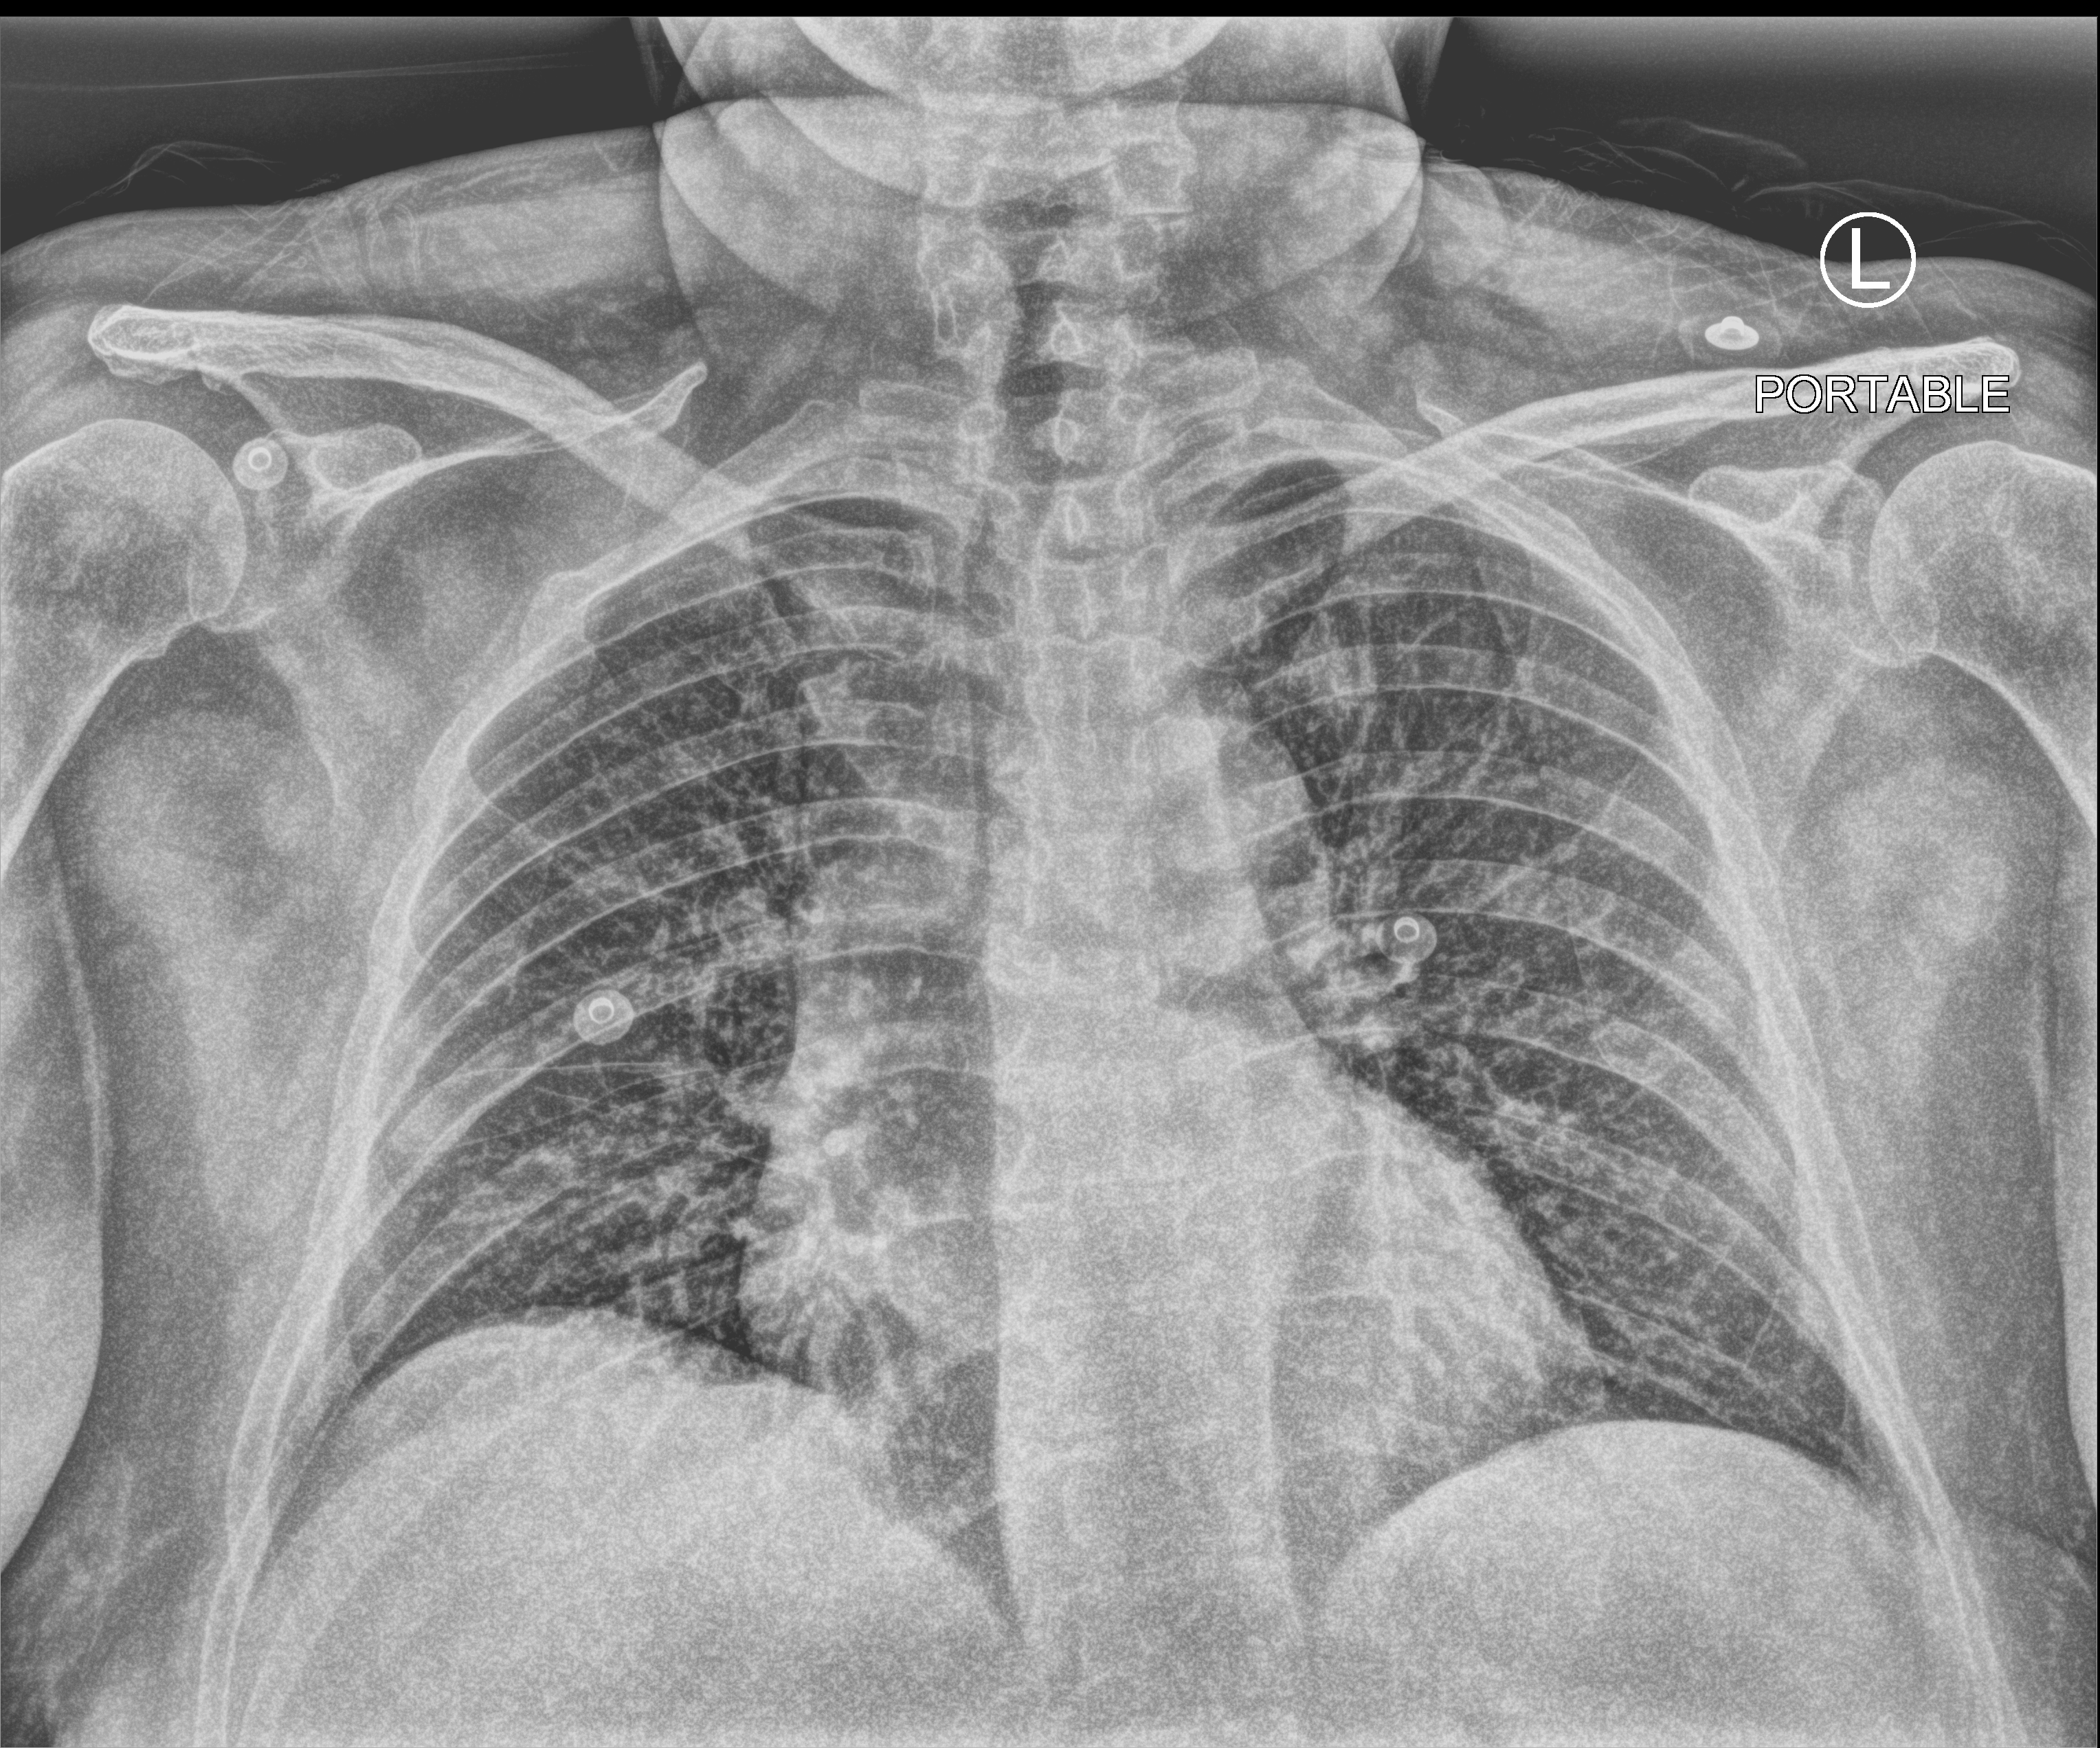
Chest X-ray (portable); anteroposterior (AP) projection. Female patient hospitalised with COVID-19, age 60–74 years.
Hospital-stay facts (about this admission, not read from this image; timing relative to this image not recorded):
- length of hospital stay: 2 days
- mechanically ventilated during this hospital stay: no
- smoking status (admission record): never